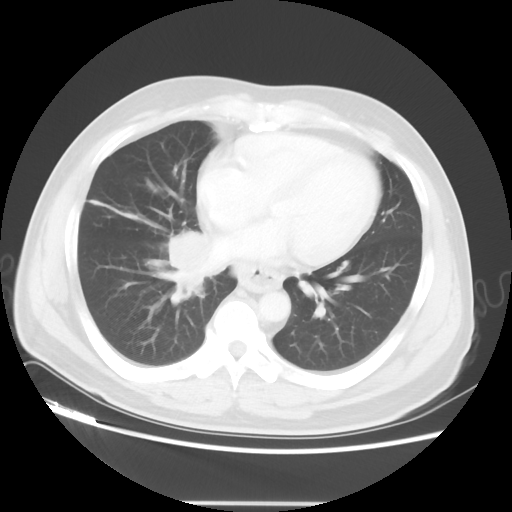
Chest CT, one axial slice; slice 20 of 48 in the series (ordered by position); reconstruction kernel STANDARD; 120 kVp; lung window (W 1500 / L -600 HU); 5 mm slice thickness; 512 × 512 image matrix, field of view 390 × 390 mm. Male patient, age 53 years. Case-level facts recorded for this patient, not image findings: clinical TNM (as recorded): T2 N3 M0; histopathological grade: G3.
Outlined on this slice (rectangle marked by the reading radiologist):
- lung tumour (recorded histology: small cell carcinoma): bounding box <157,227,213,297> (left, top, right, bottom; pixels)